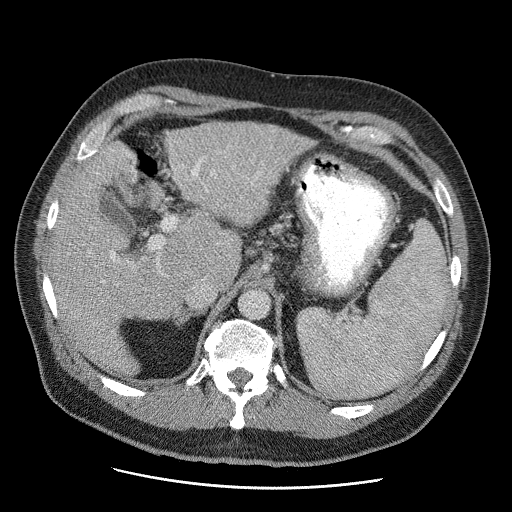
Contrast-enhanced abdominal CT (liver protocol), one axial slice; position 33 of 81 along the scan axis; 120 kVp; soft-tissue window (W 400 / L 40 HU); 2.5 mm slice thickness; 512 × 512 image matrix. Case-level facts recorded for this patient, not image findings: diagnosis: hepatocellular carcinoma (patient treated with transarterial chemoembolisation; whether this scan precedes or follows treatment is not stated here); TNM stage (as recorded): Stage-IIIA; Child-Pugh class: A; tumour differentiation: moderately differentiated.
Annotated regions visible in this slice (semi-automatic segmentation, software-assisted and operator-edited):
- liver parenchyma outside the tumour (the mass and vessels are separate outlines, so this box may not span the whole liver): bounding box (x1, y1, x2, y2) in pixels: (48, 122, 312, 370)
- liver vessels: (111, 161, 212, 259)